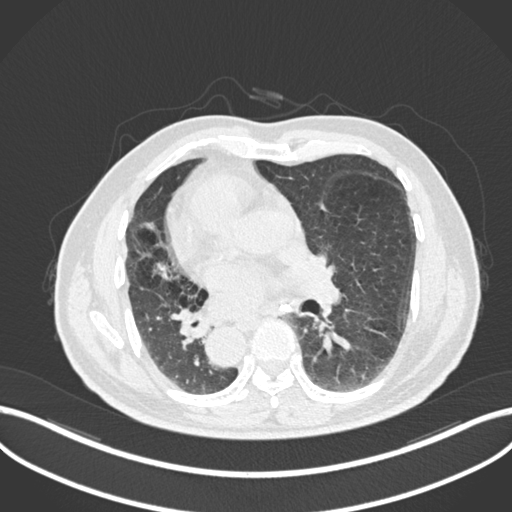
Chest CT, one axial slice; slice 107 of 206 in the series (ordered by position); reconstruction kernel B30f; 120 kVp; lung window (W 1500 / L -600 HU); 1 mm slice thickness; 512 × 512 image matrix. Male patient, age 67 years. Case-level facts recorded for this patient, not image findings: clinical TNM (as recorded): T2a N0 M0.
Annotated regions visible in this slice (bounding box drawn by a radiologist):
- lung tumour (recorded histology: squamous cell carcinoma): box from (x=162, y=302) to (x=216, y=343) px